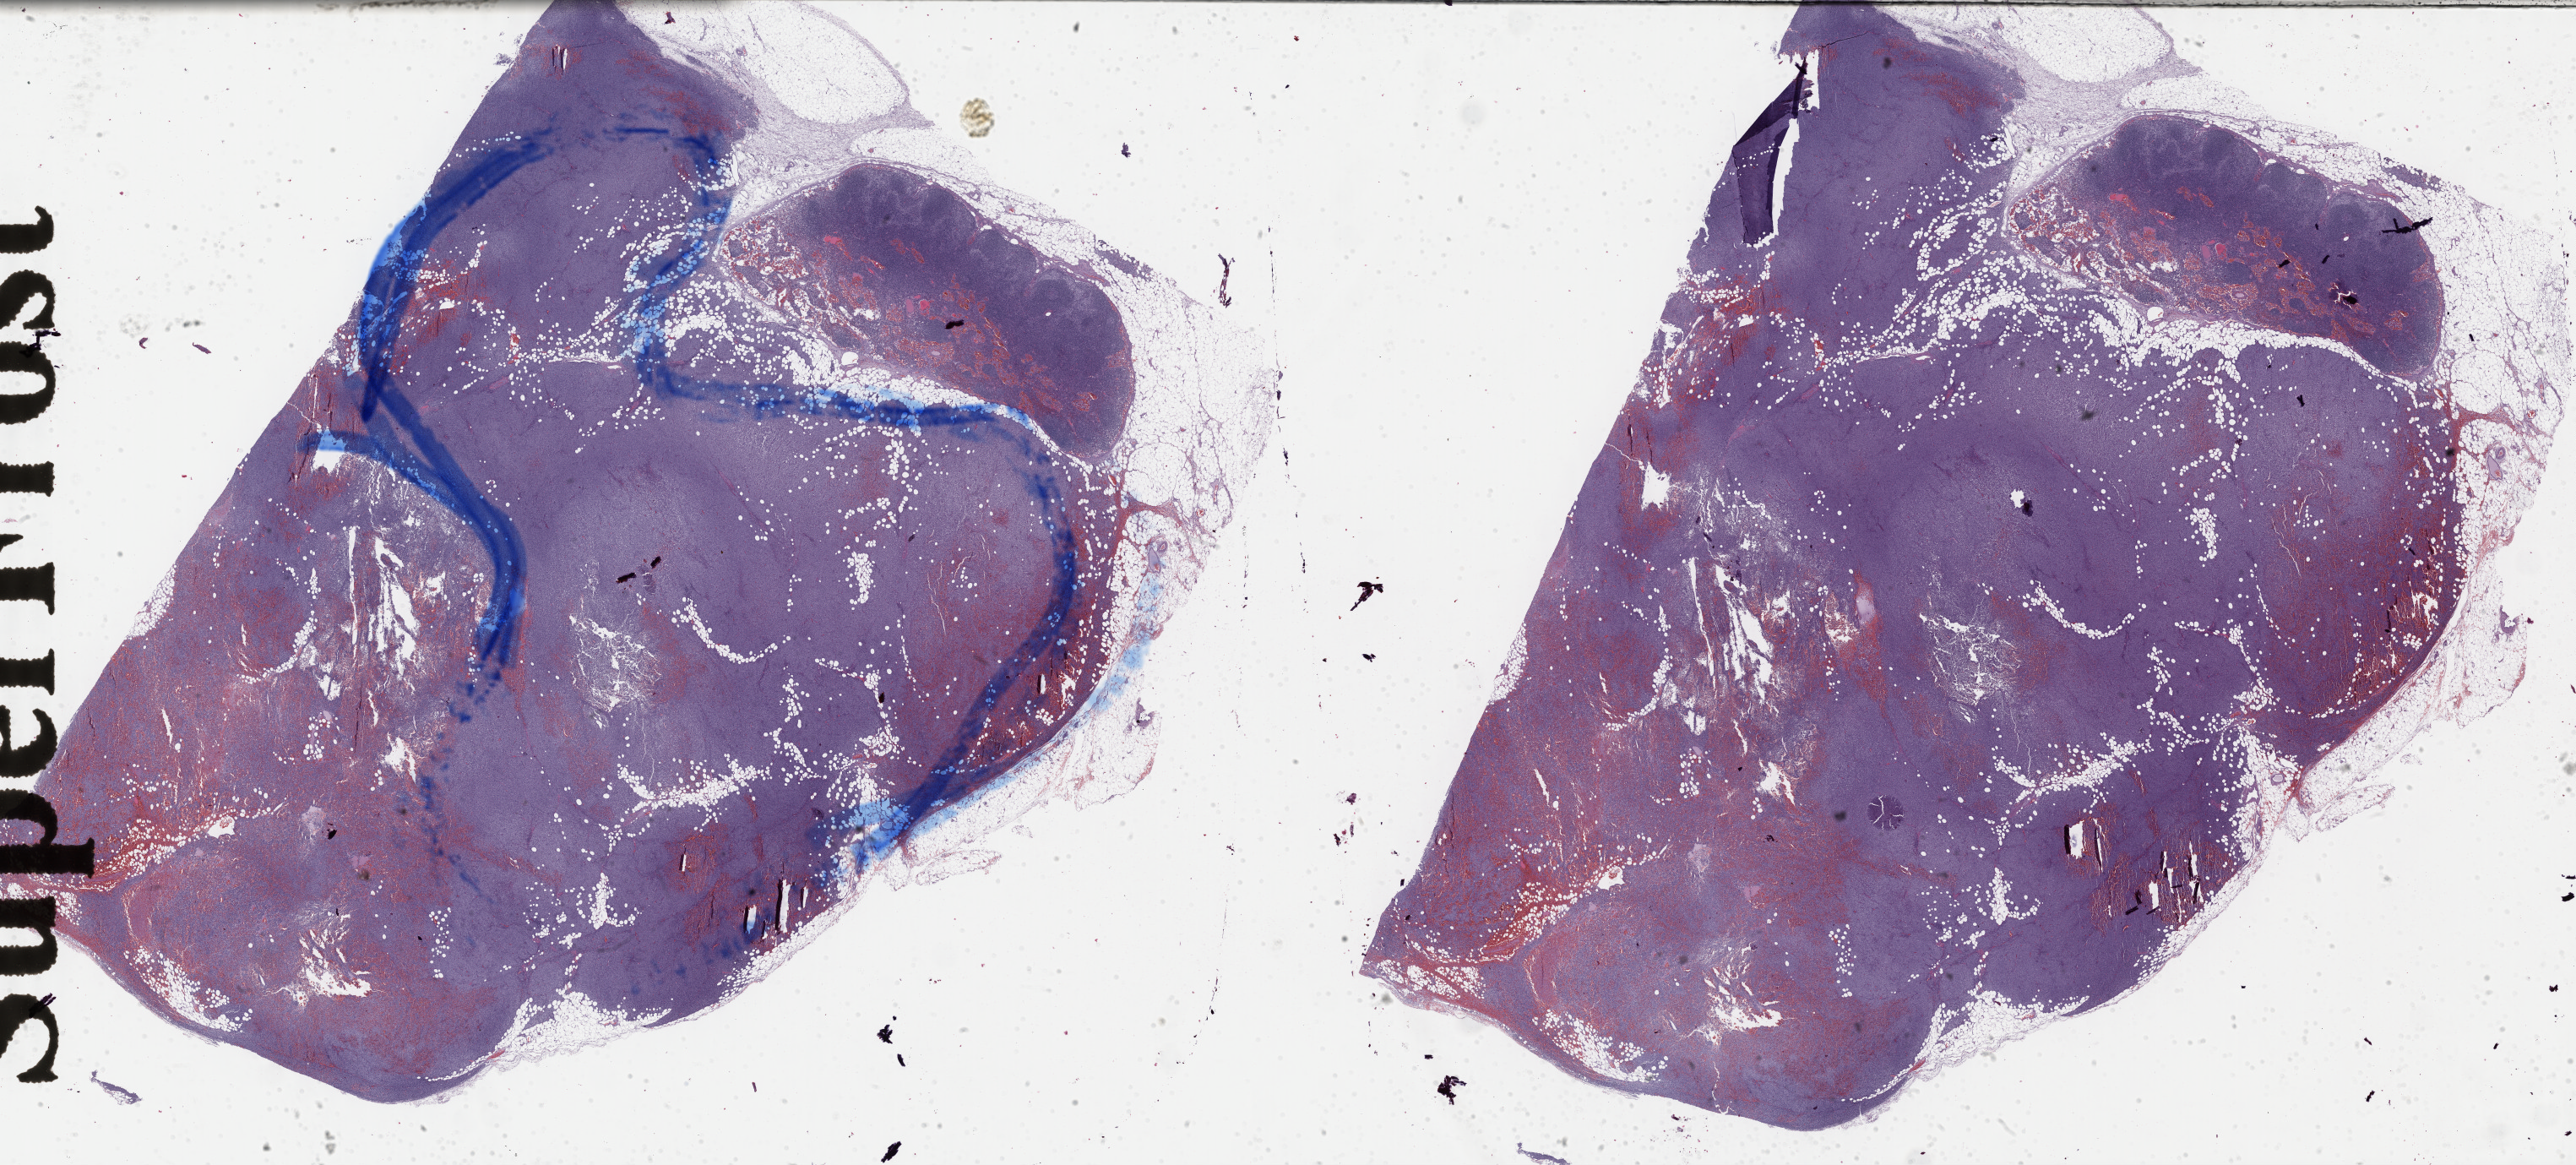
Whole-slide histology image, H&E — whole scanned area (about 49.3 x 22.3 mm, slide scanned at 40x) shown as a low-resolution overview. Formalin-fixed paraffin-embedded (FFPE) diagnostic section. Skin, primary tumour sample. Patient: male, age at initial diagnosis 58 years.
* histologic diagnosis: Malignant melanoma, NOS